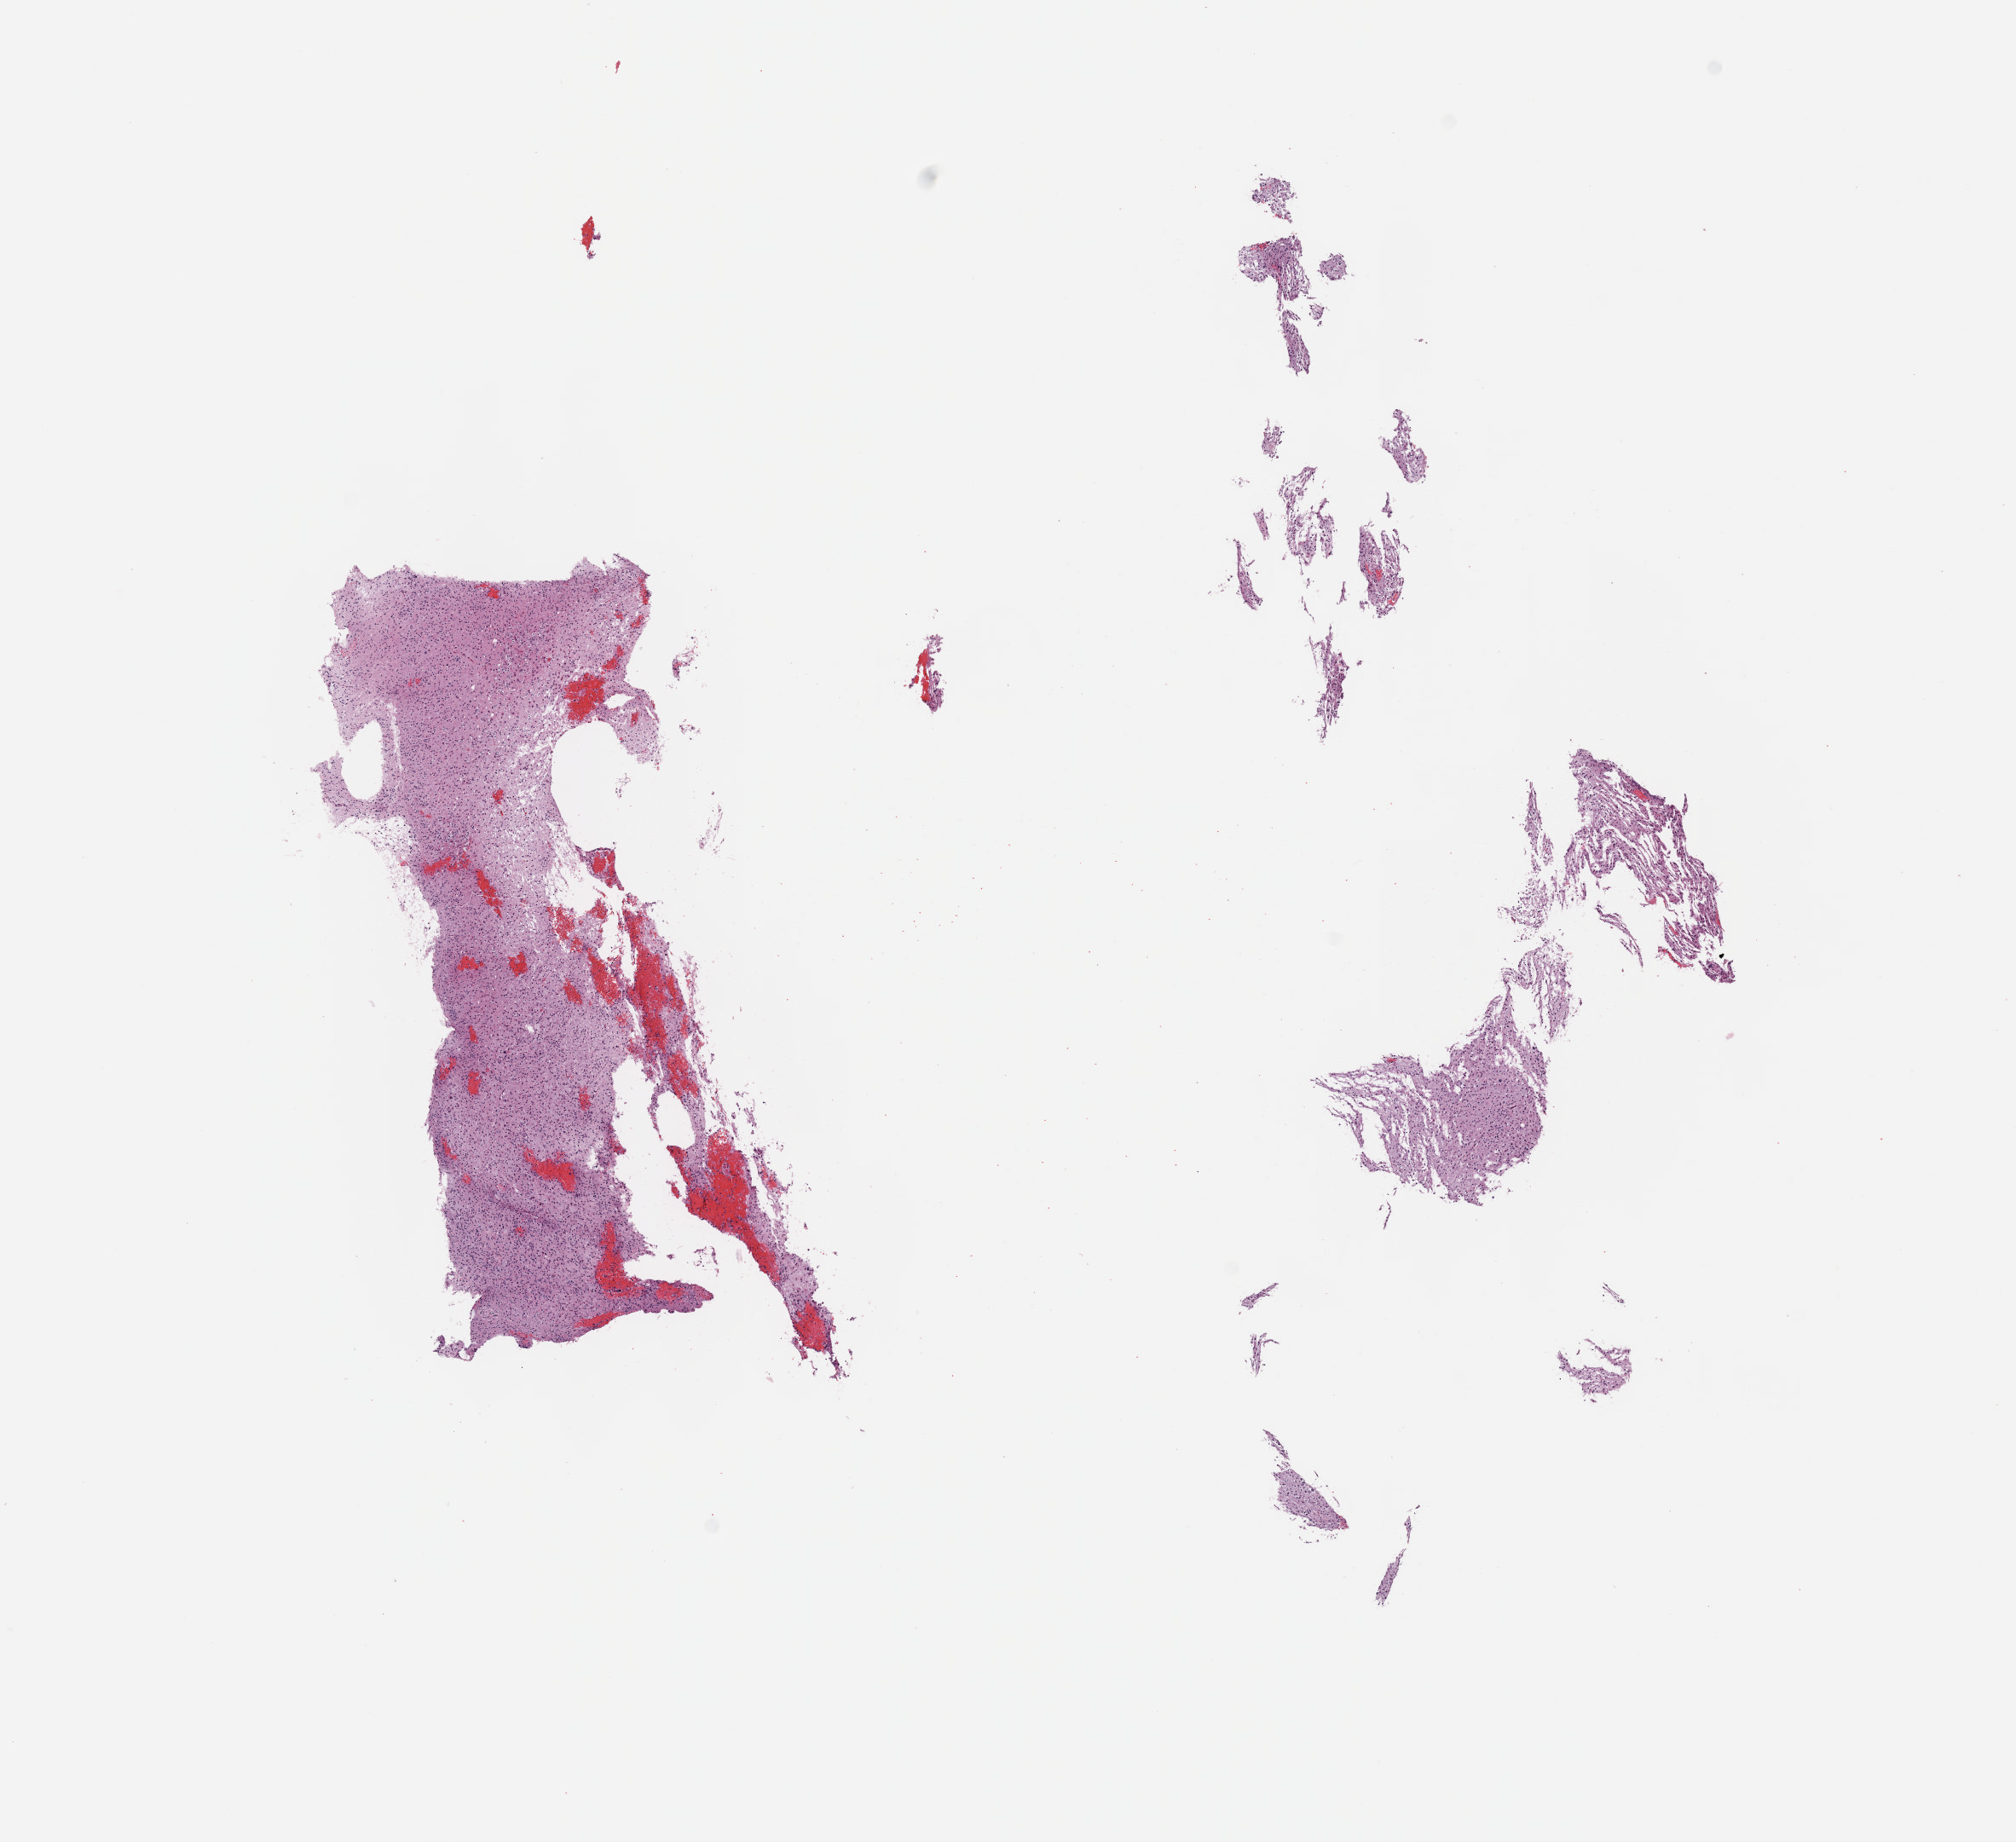
Digitized H&E-stained tissue section (whole slide) — a low-resolution overview of the entire scanned area, about 9.6 x 8.7 mm; formalin-fixed paraffin-embedded (FFPE) diagnostic section; sample: primary tumour, brain. Patient: male, age at initial diagnosis 26 years. Histologic grade: G2 (moderately differentiated).
• histologic diagnosis: Oligodendroglioma, NOS (cerebrum)
• laterality: left